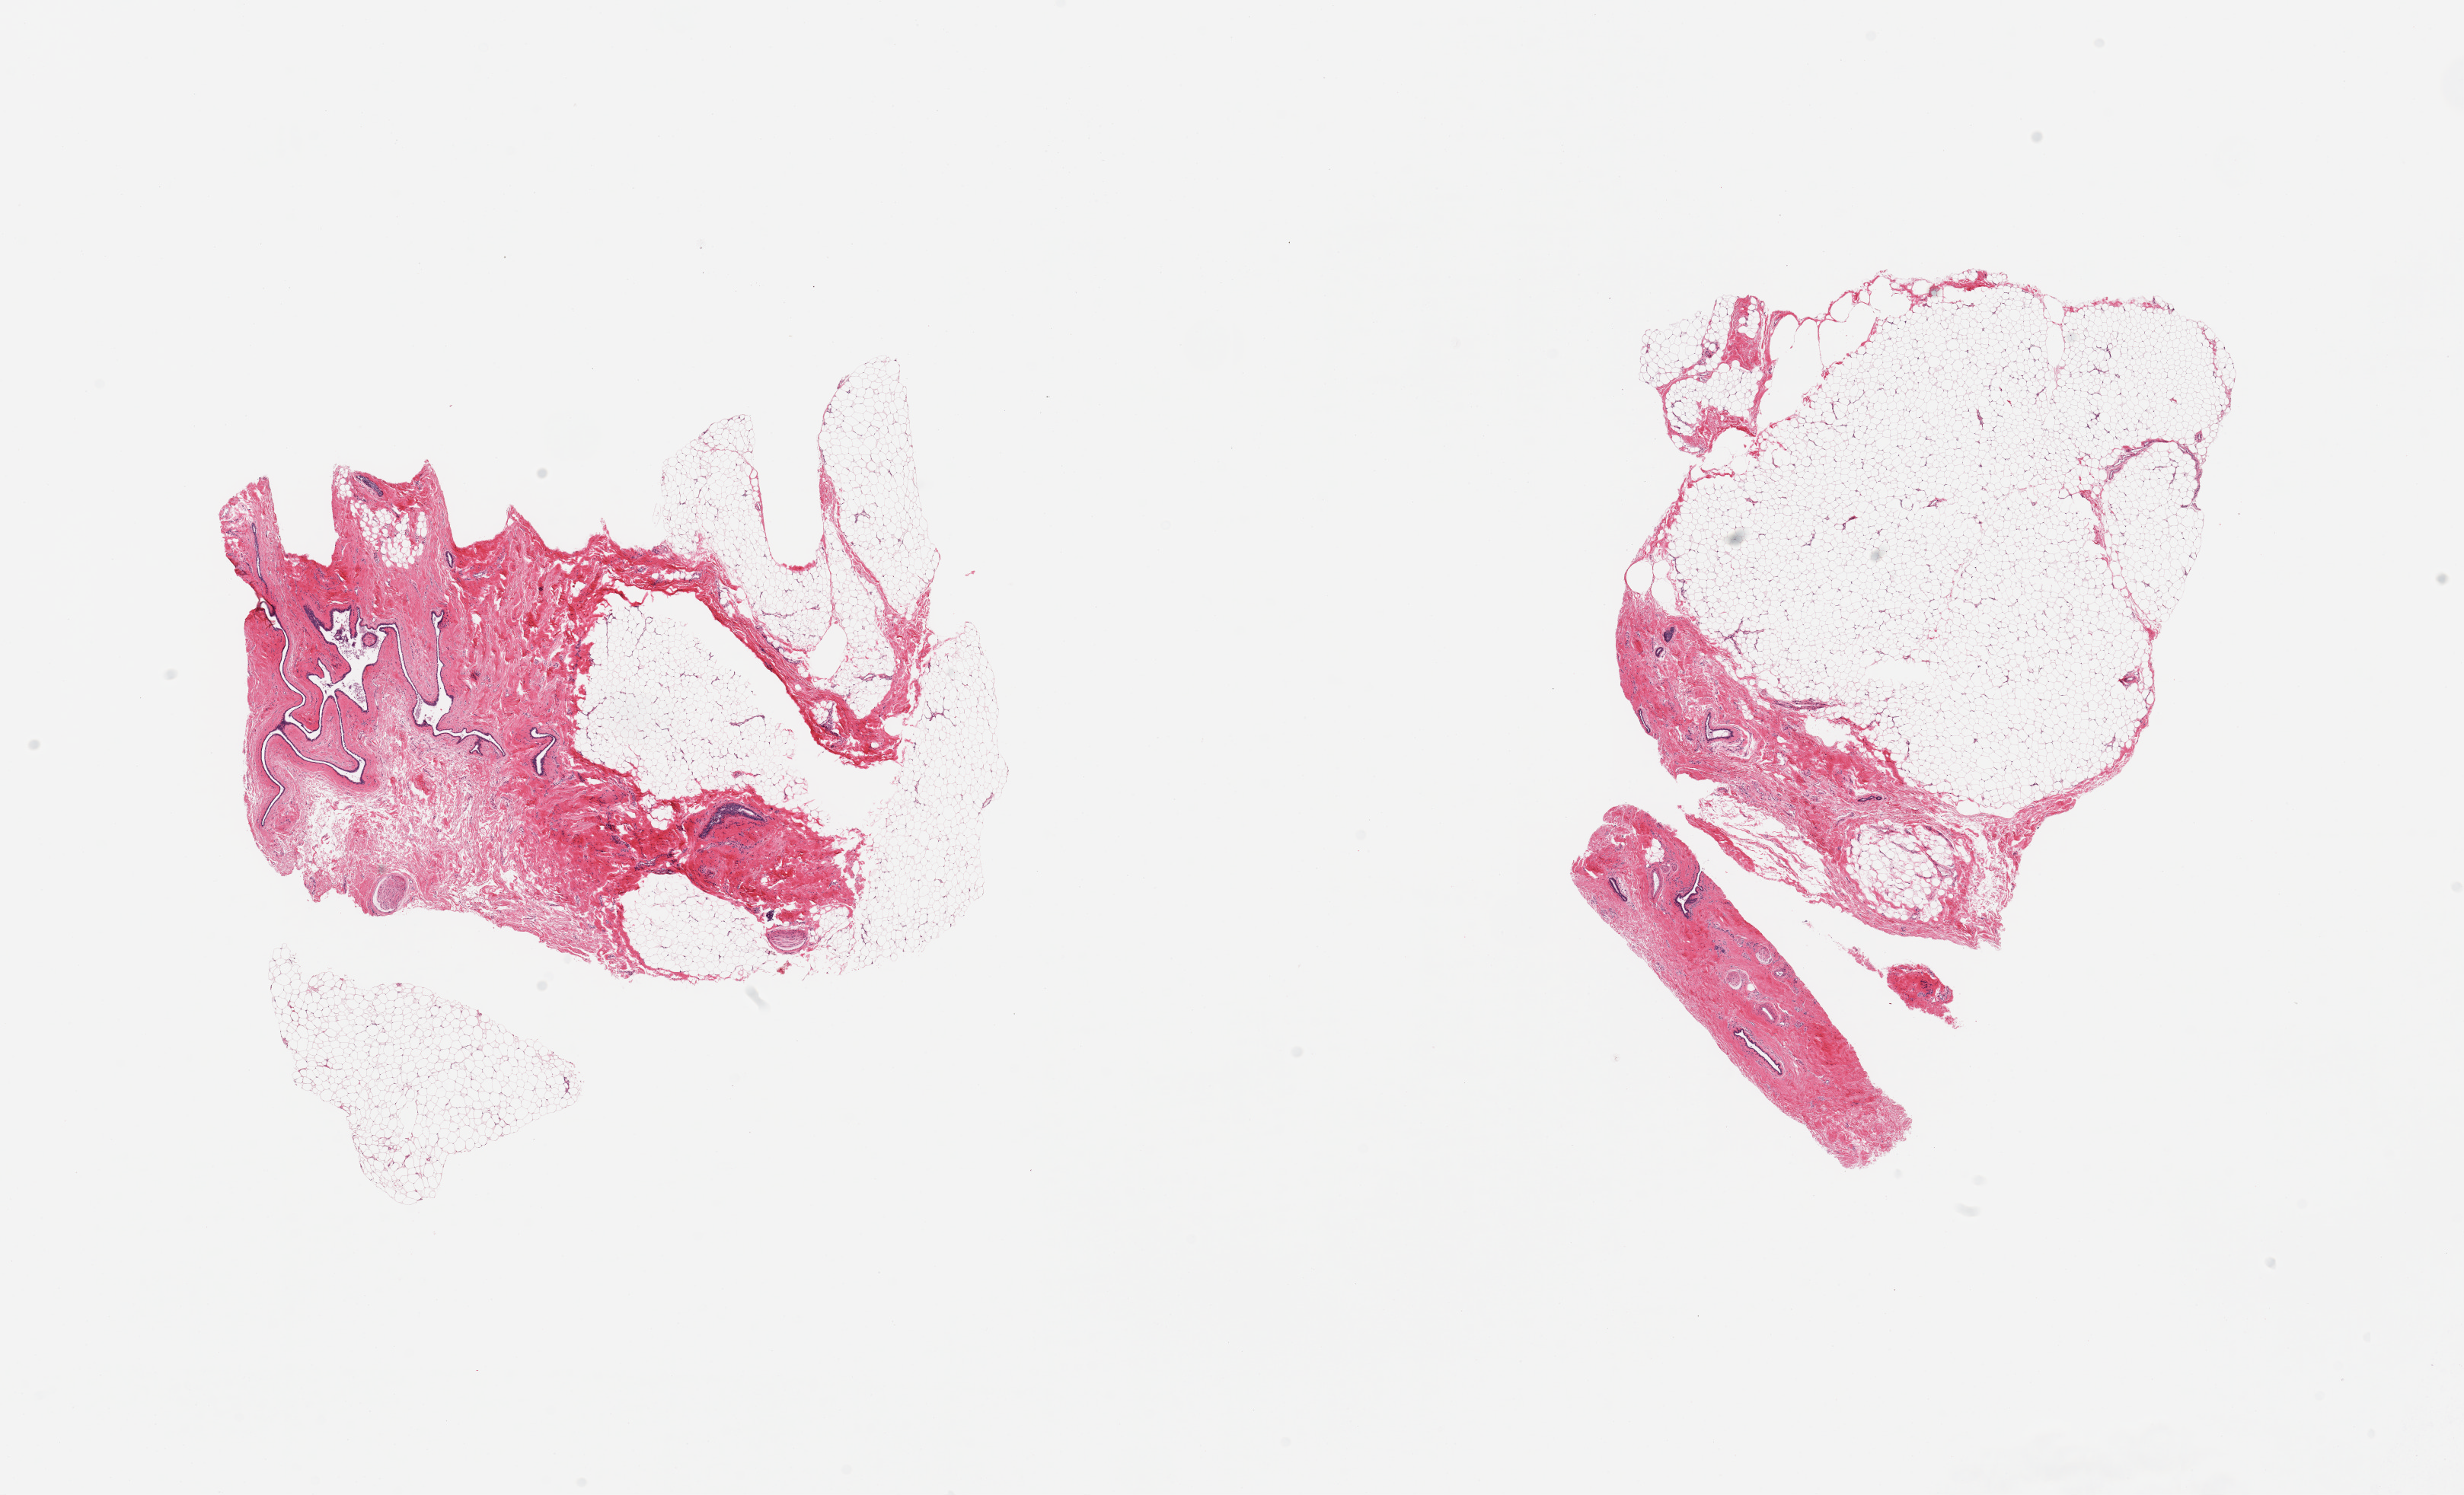
Whole-slide image, haematoxylin and eosin stain, shown as a low-resolution overview of the whole scanned area (about 25.6 x 15.5 mm, acquisition: 20x scan); PAXgene-fixed paraffin-embedded (PFPE) section; section of breast (target tissue); tissue donor sample. Male donor.
Pathologist's review note for this sample: 2 pieces gynecomastoid stromal and ductal hyperplasia.